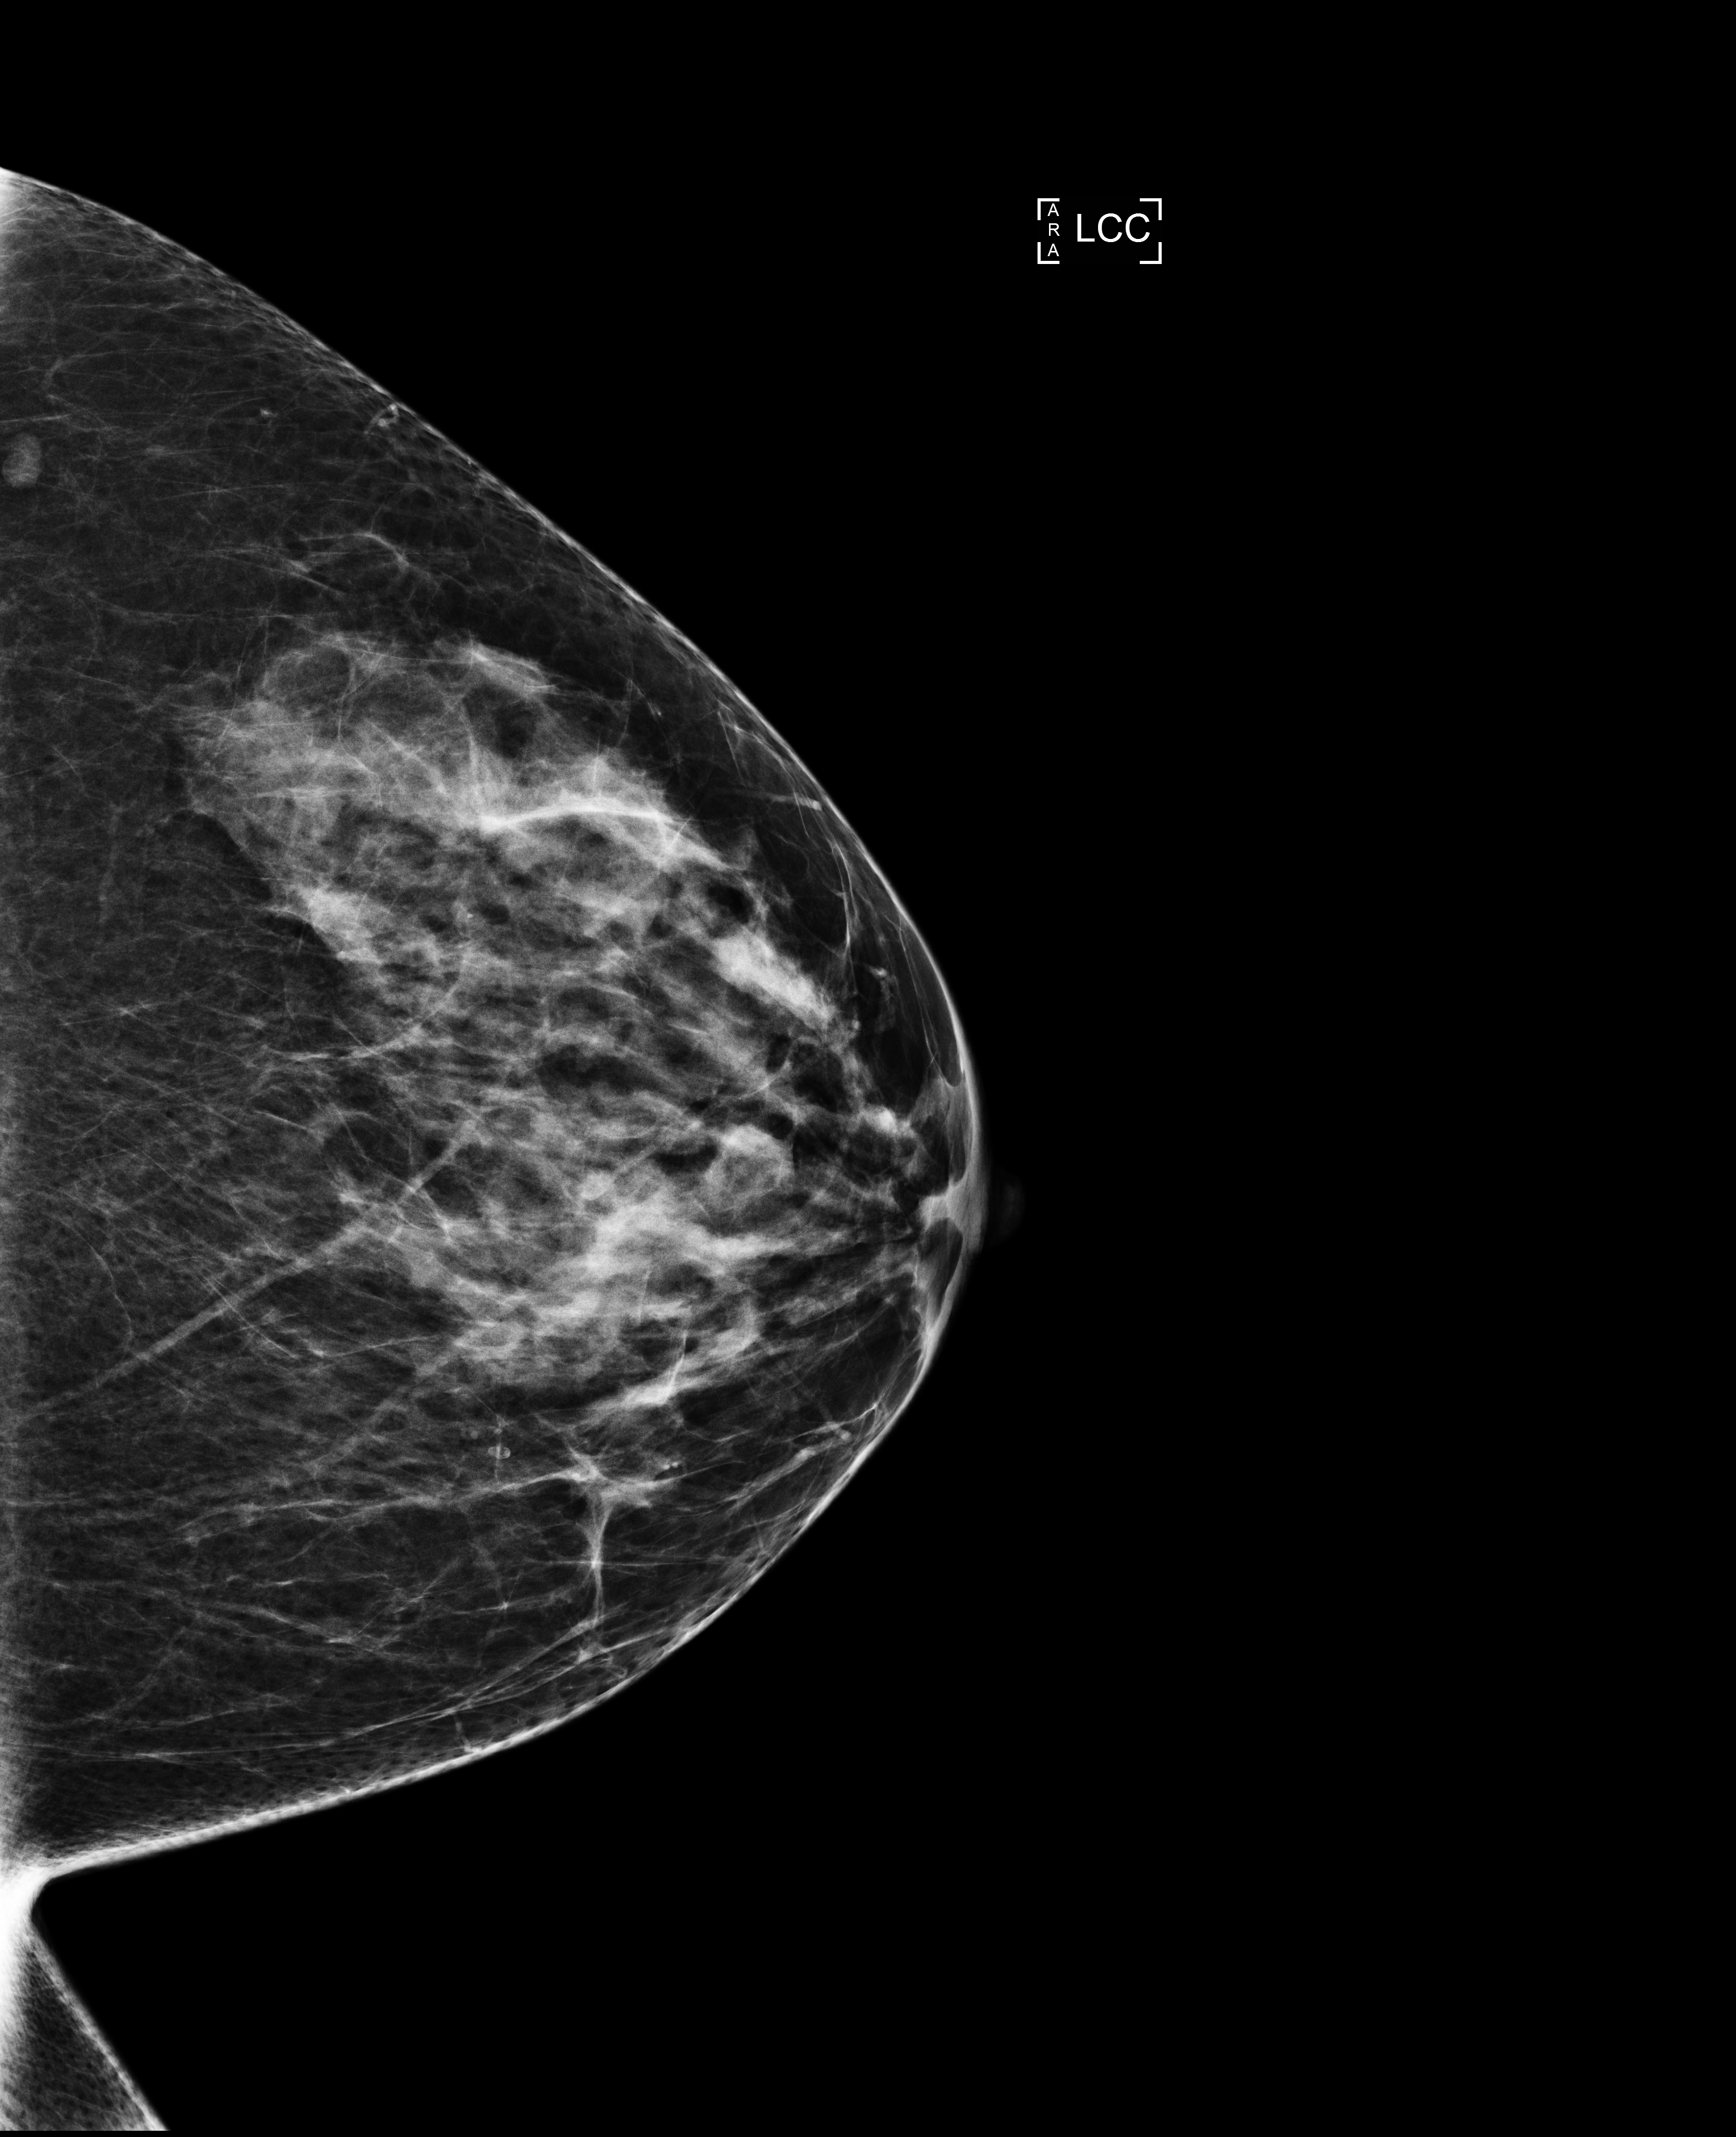
Annual screening mammography examination, system: Selenia Dimensions. Patient: female, 51 years.
Image type: full-field digital mammogram. Breast: left. Projection: CC view. Breast density at the screening exam (both breasts): heterogeneously dense (BI-RADS density category c). Final BI-RADS category for the screening round (tomosynthesis exam, both breasts): category 1. Recall: no recall after this screen.